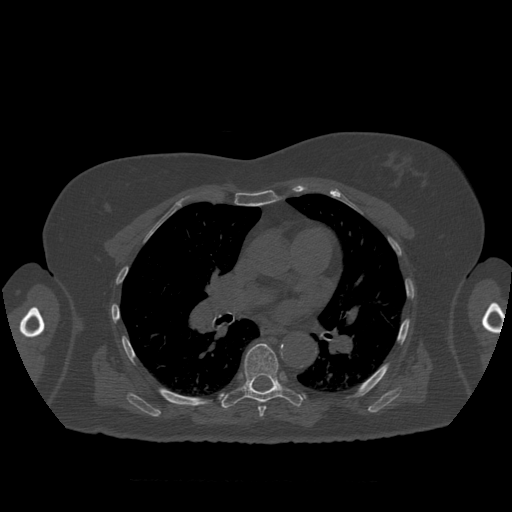
CT including the spine, one axial slice. Slice 399 of 399 in the series (ordered by position). Reconstruction kernel STANDARD. 120 kVp. Bone window (W 1800 / L 400 HU). 512 × 512 image matrix, field of view 404 × 404 mm. Patient age 81 years. From the clinical record (not read from this slice): primary cancer: renal.
Annotated regions visible in this slice (semi-automatic segmentation, software-assisted and operator-edited):
- T7 vertebra: bounding box <219,344,304,417> (left, top, right, bottom; pixels)